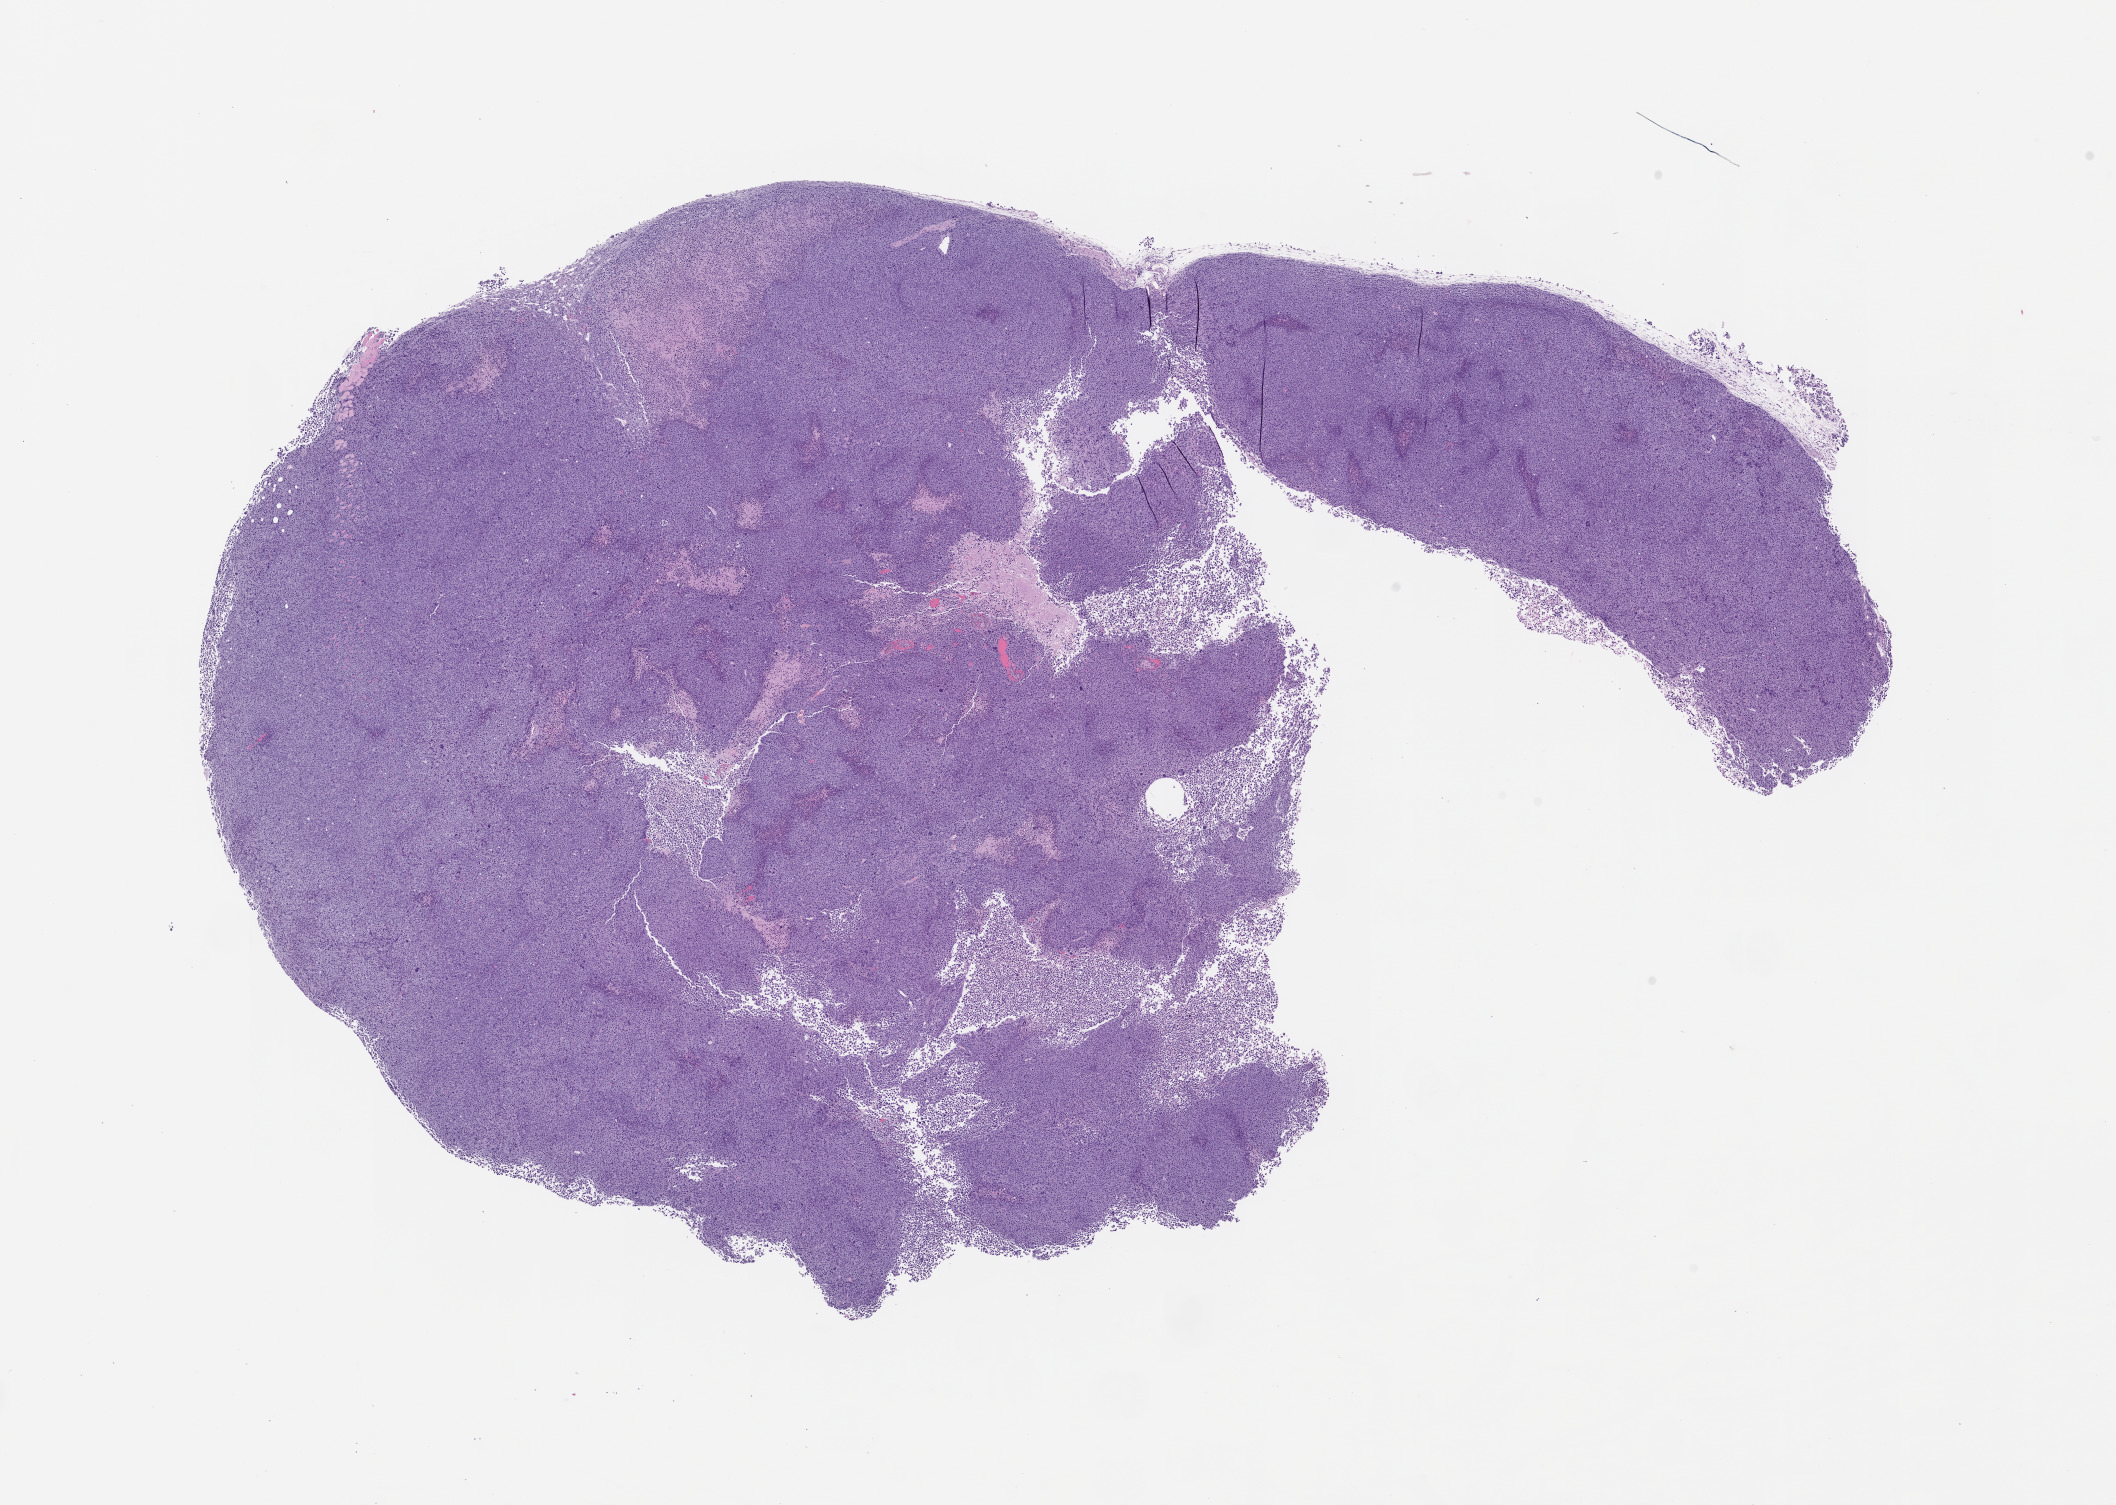
Whole-slide image, H&E: patient-derived xenograft (human tumor grown in a mouse), passage 5 — shown as a low-resolution overview of the whole scanned area (about 17.0 x 12.1 mm). Formalin-fixed paraffin-embedded section. Originating tumor site category: bladder.
Originating patient diagnosis: Urothelial Carcinoma.